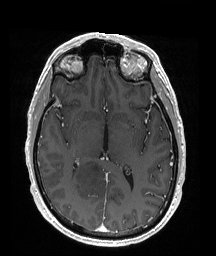
Brain MRI from a brain-tumour surgery series, one axial slice; slice 98 of 176 in the series (ordered by position); T1-weighted post-contrast; 1 mm slice thickness; 216 × 256 image matrix, field of view 211 × 250 mm. Case-level facts recorded for this patient, not image findings: histopathology: Oligodendroglioma; WHO grade: 2; IDH mutation: yes.
Outlined on this slice (expert manual segmentation):
- tumour: bounding box [x1, y1, x2, y2] px = [70, 157, 111, 194]